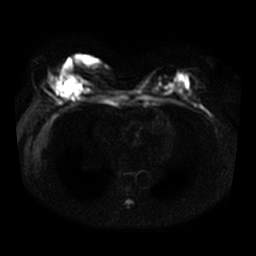
Breast MRI, one axial slice. Slice 17 of 36 in the series (ordered by position). Diffusion-weighted series; image 2 of 4 stored at this slice position (different b-values; order by instance number). 3 T. 5 mm slice thickness. 256 × 256 image matrix, field of view 330 × 330 mm. Female patient.
Outlined on this slice (outlined manually by an expert reader):
- tumour on diffusion-weighted imaging: box from (x=64, y=76) to (x=80, y=96) px